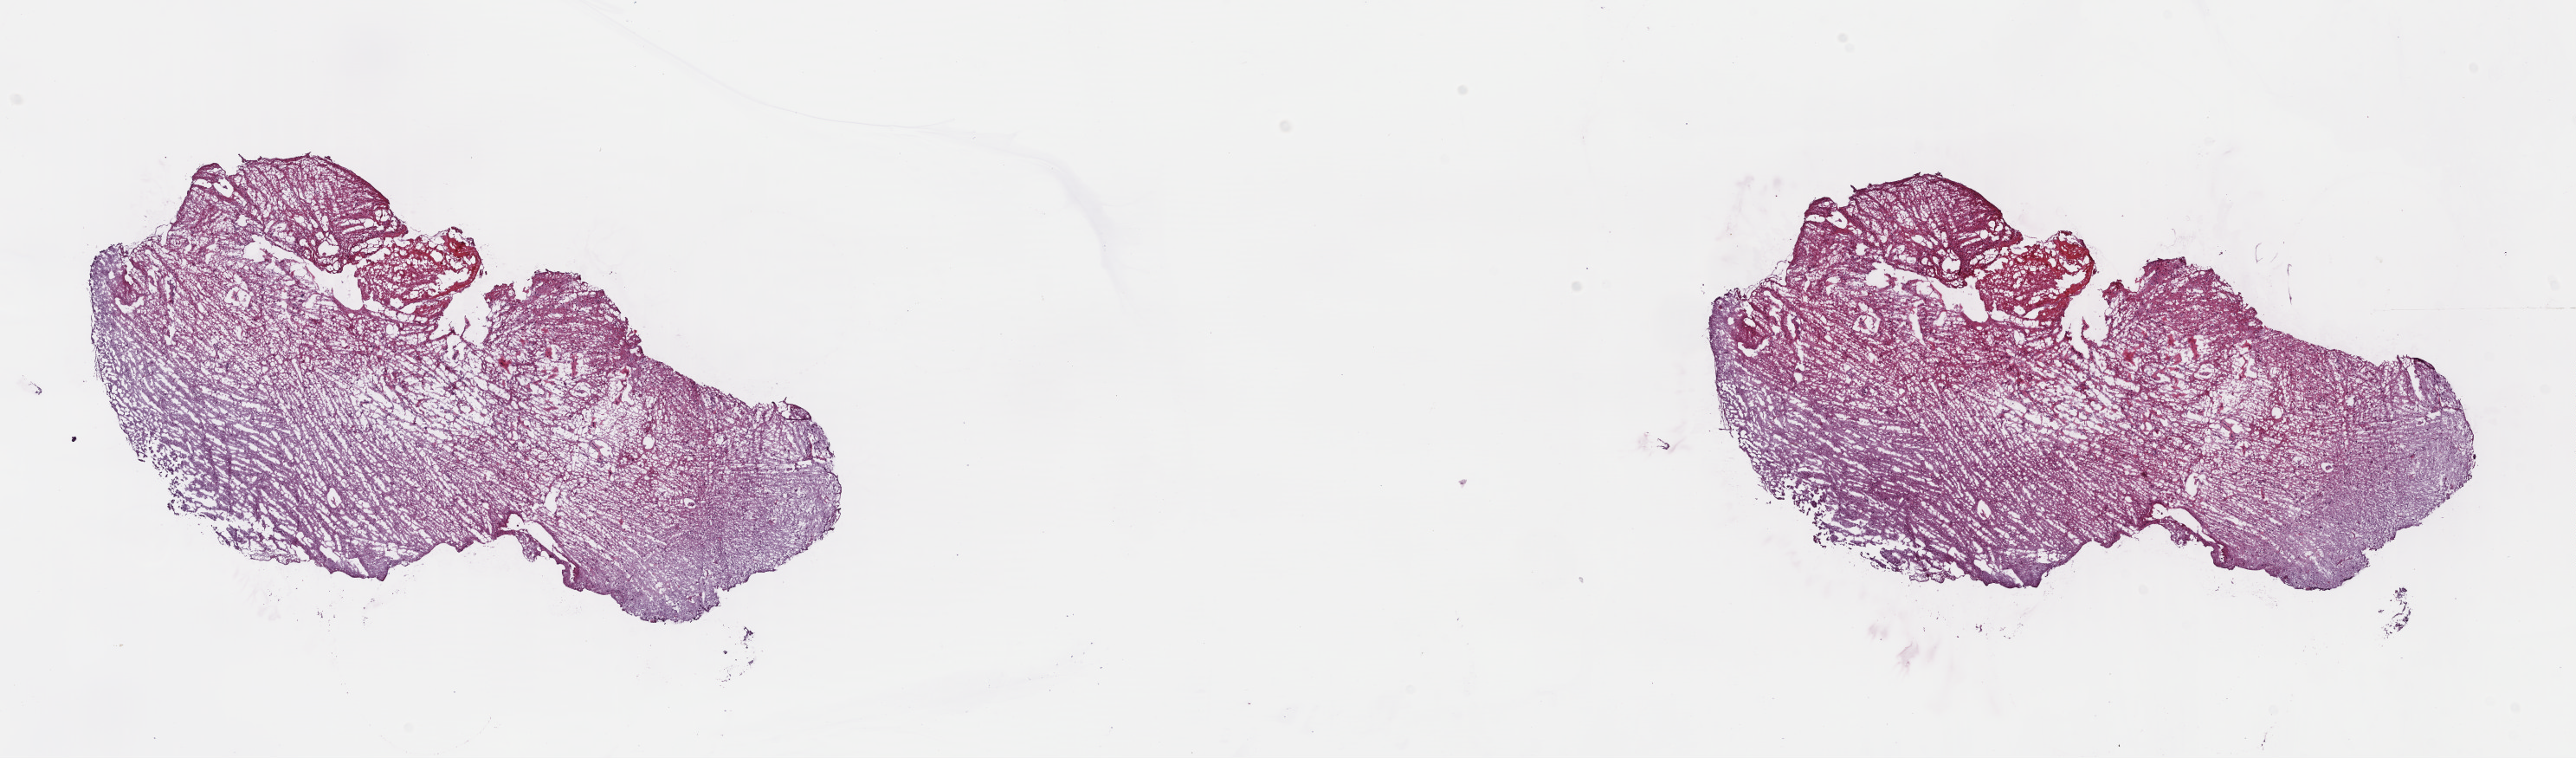
Whole-slide histology image, H&E, whole scanned area (about 23.4 x 6.9 mm, slide scanned at 40x) shown as a low-resolution overview, frozen section from the top of the tissue portion, sample: primary tumour, brain. Patient: female, age at initial diagnosis 41 years. Histologic grade: G3 (poorly differentiated). Pathologist review of this section (percent, as recorded): tumour cells 30%, tumour nuclei 70%, normal cells 10%, stromal cells 60%, necrosis 0%. Infiltration values recorded for this section: lymphocyte infiltration 0%, monocyte infiltration 0%, neutrophil infiltration 0%.
Laterality: right. Diagnosis: Oligodendroglioma, anaplastic (cerebrum).